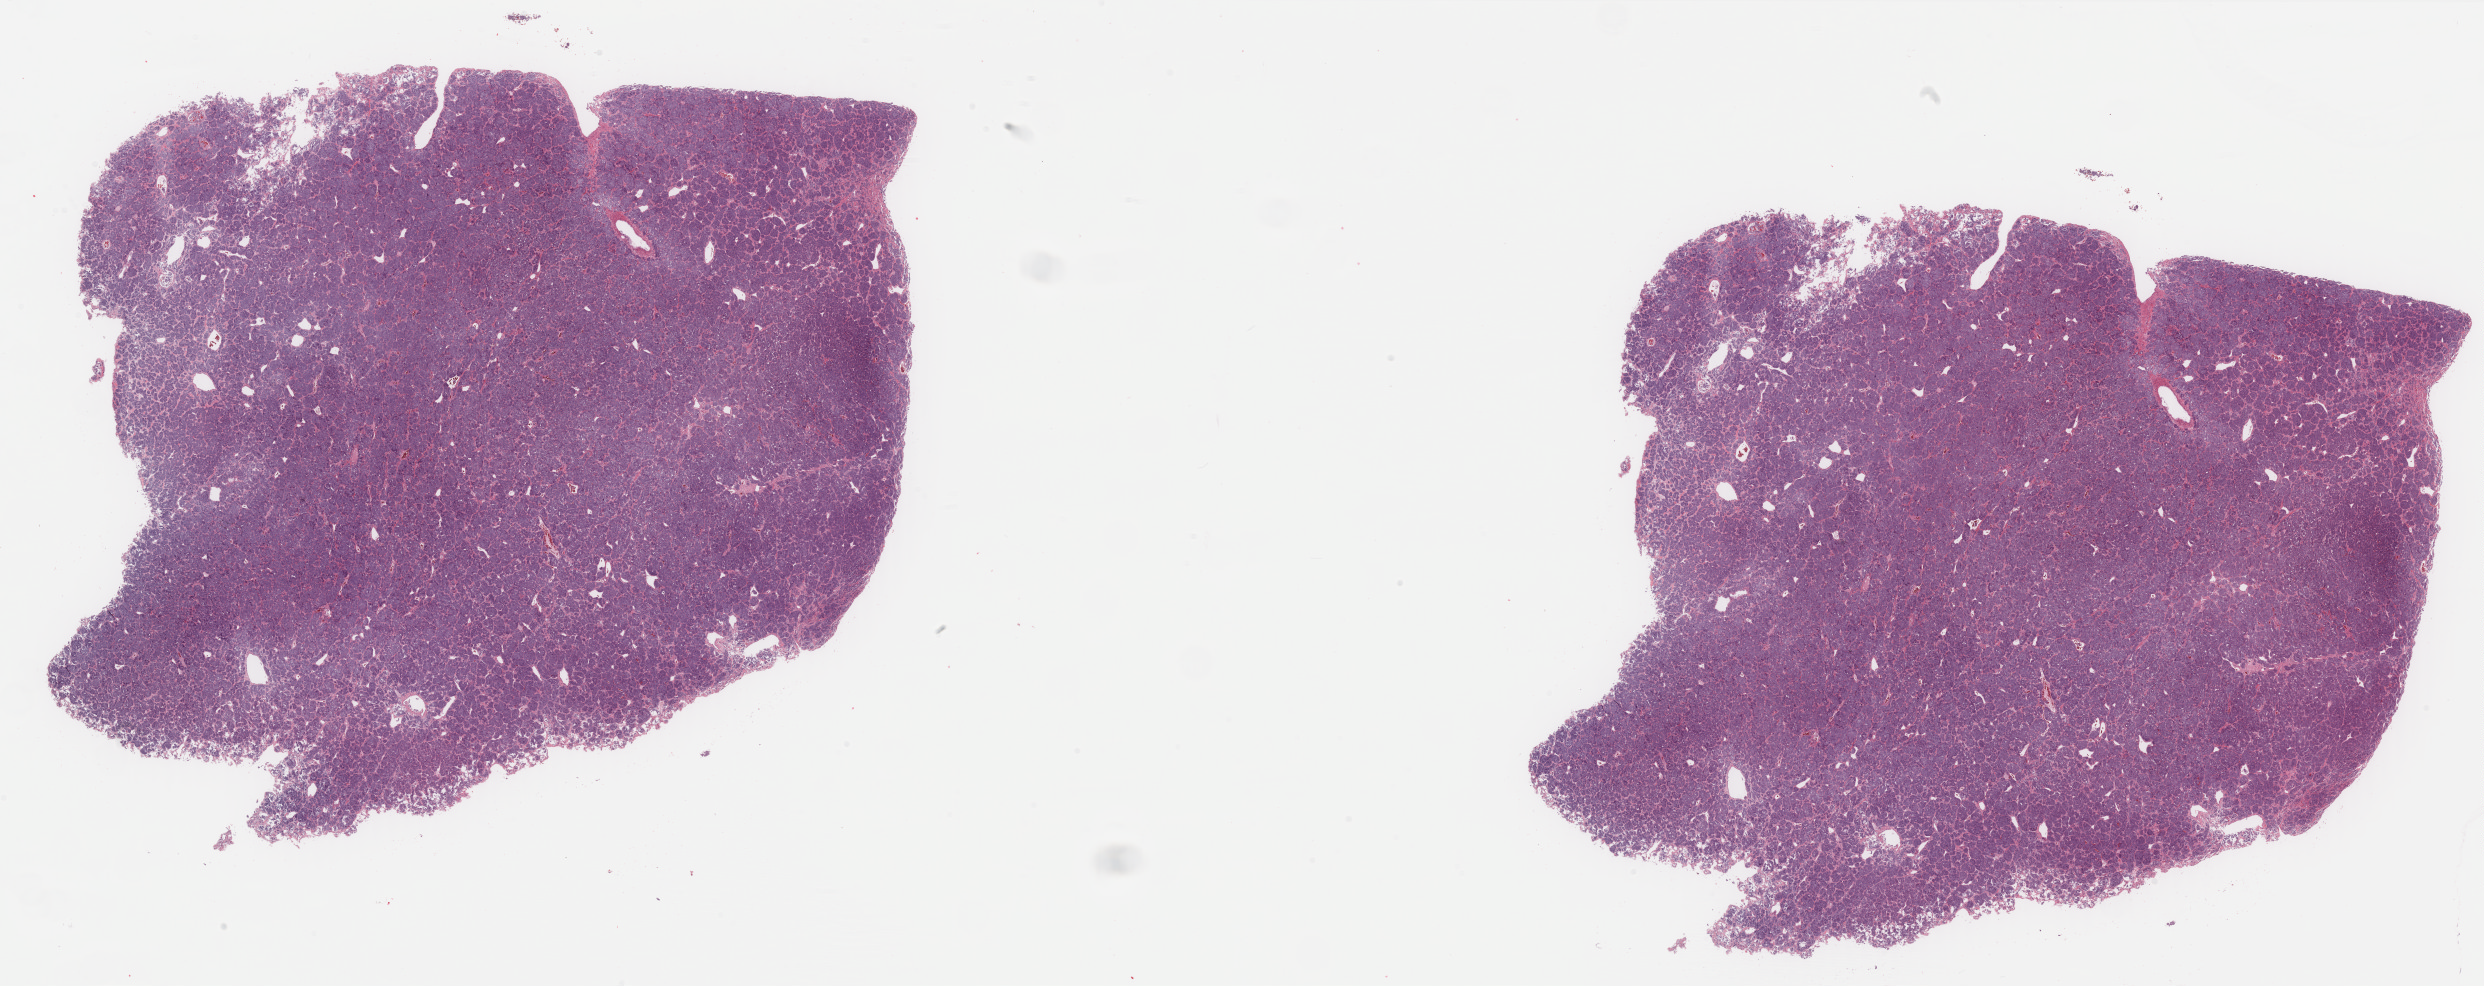
Digitized H&E tissue section (whole slide), a low-resolution overview of the entire scanned area, about 39.3 x 15.6 mm. FFPE section. Sample: primary tumour, adrenal gland. Female patient; age at initial diagnosis 56 years.
Diagnosis: Pheochromocytoma, malignant.